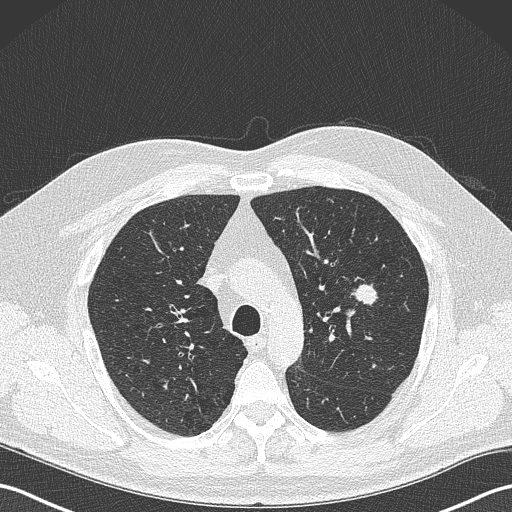
Low-dose screening chest CT, one axial slice. Slice 246 of 343 in the series (ordered by position). Reconstruction kernel B50f. Lung window (W 1500 / L -600 HU). 1 mm slice thickness. 512 × 512 image matrix, field of view 350 × 350 mm.
Annotated regions visible in this slice (outlined manually by an expert reader):
- lesion 1 (tumor, upper lobe of left lung): bounding box <350,284,379,305> (left, top, right, bottom; pixels)